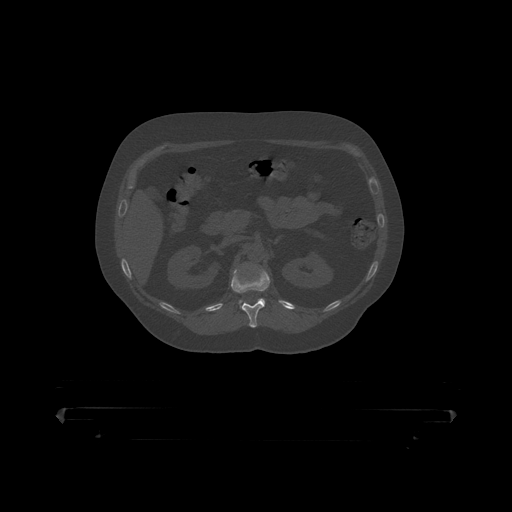
CT including the spine, one axial slice; slice 162 of 390 in the series (ordered by position); reconstruction kernel STANDARD; bone window (W 1800 / L 400 HU); 1.25 mm slice thickness; 512 × 512 image matrix, field of view 650 × 650 mm. Patient: male, 60 years. Case-level facts recorded for this patient, not image findings: primary cancer: prostate.
Annotated regions visible in this slice (semi-automatically segmented with operator editing):
- L1 vertebra: bounding box <240,299,265,308> (left, top, right, bottom; pixels)
- T12 vertebra: <232,265,270,319>